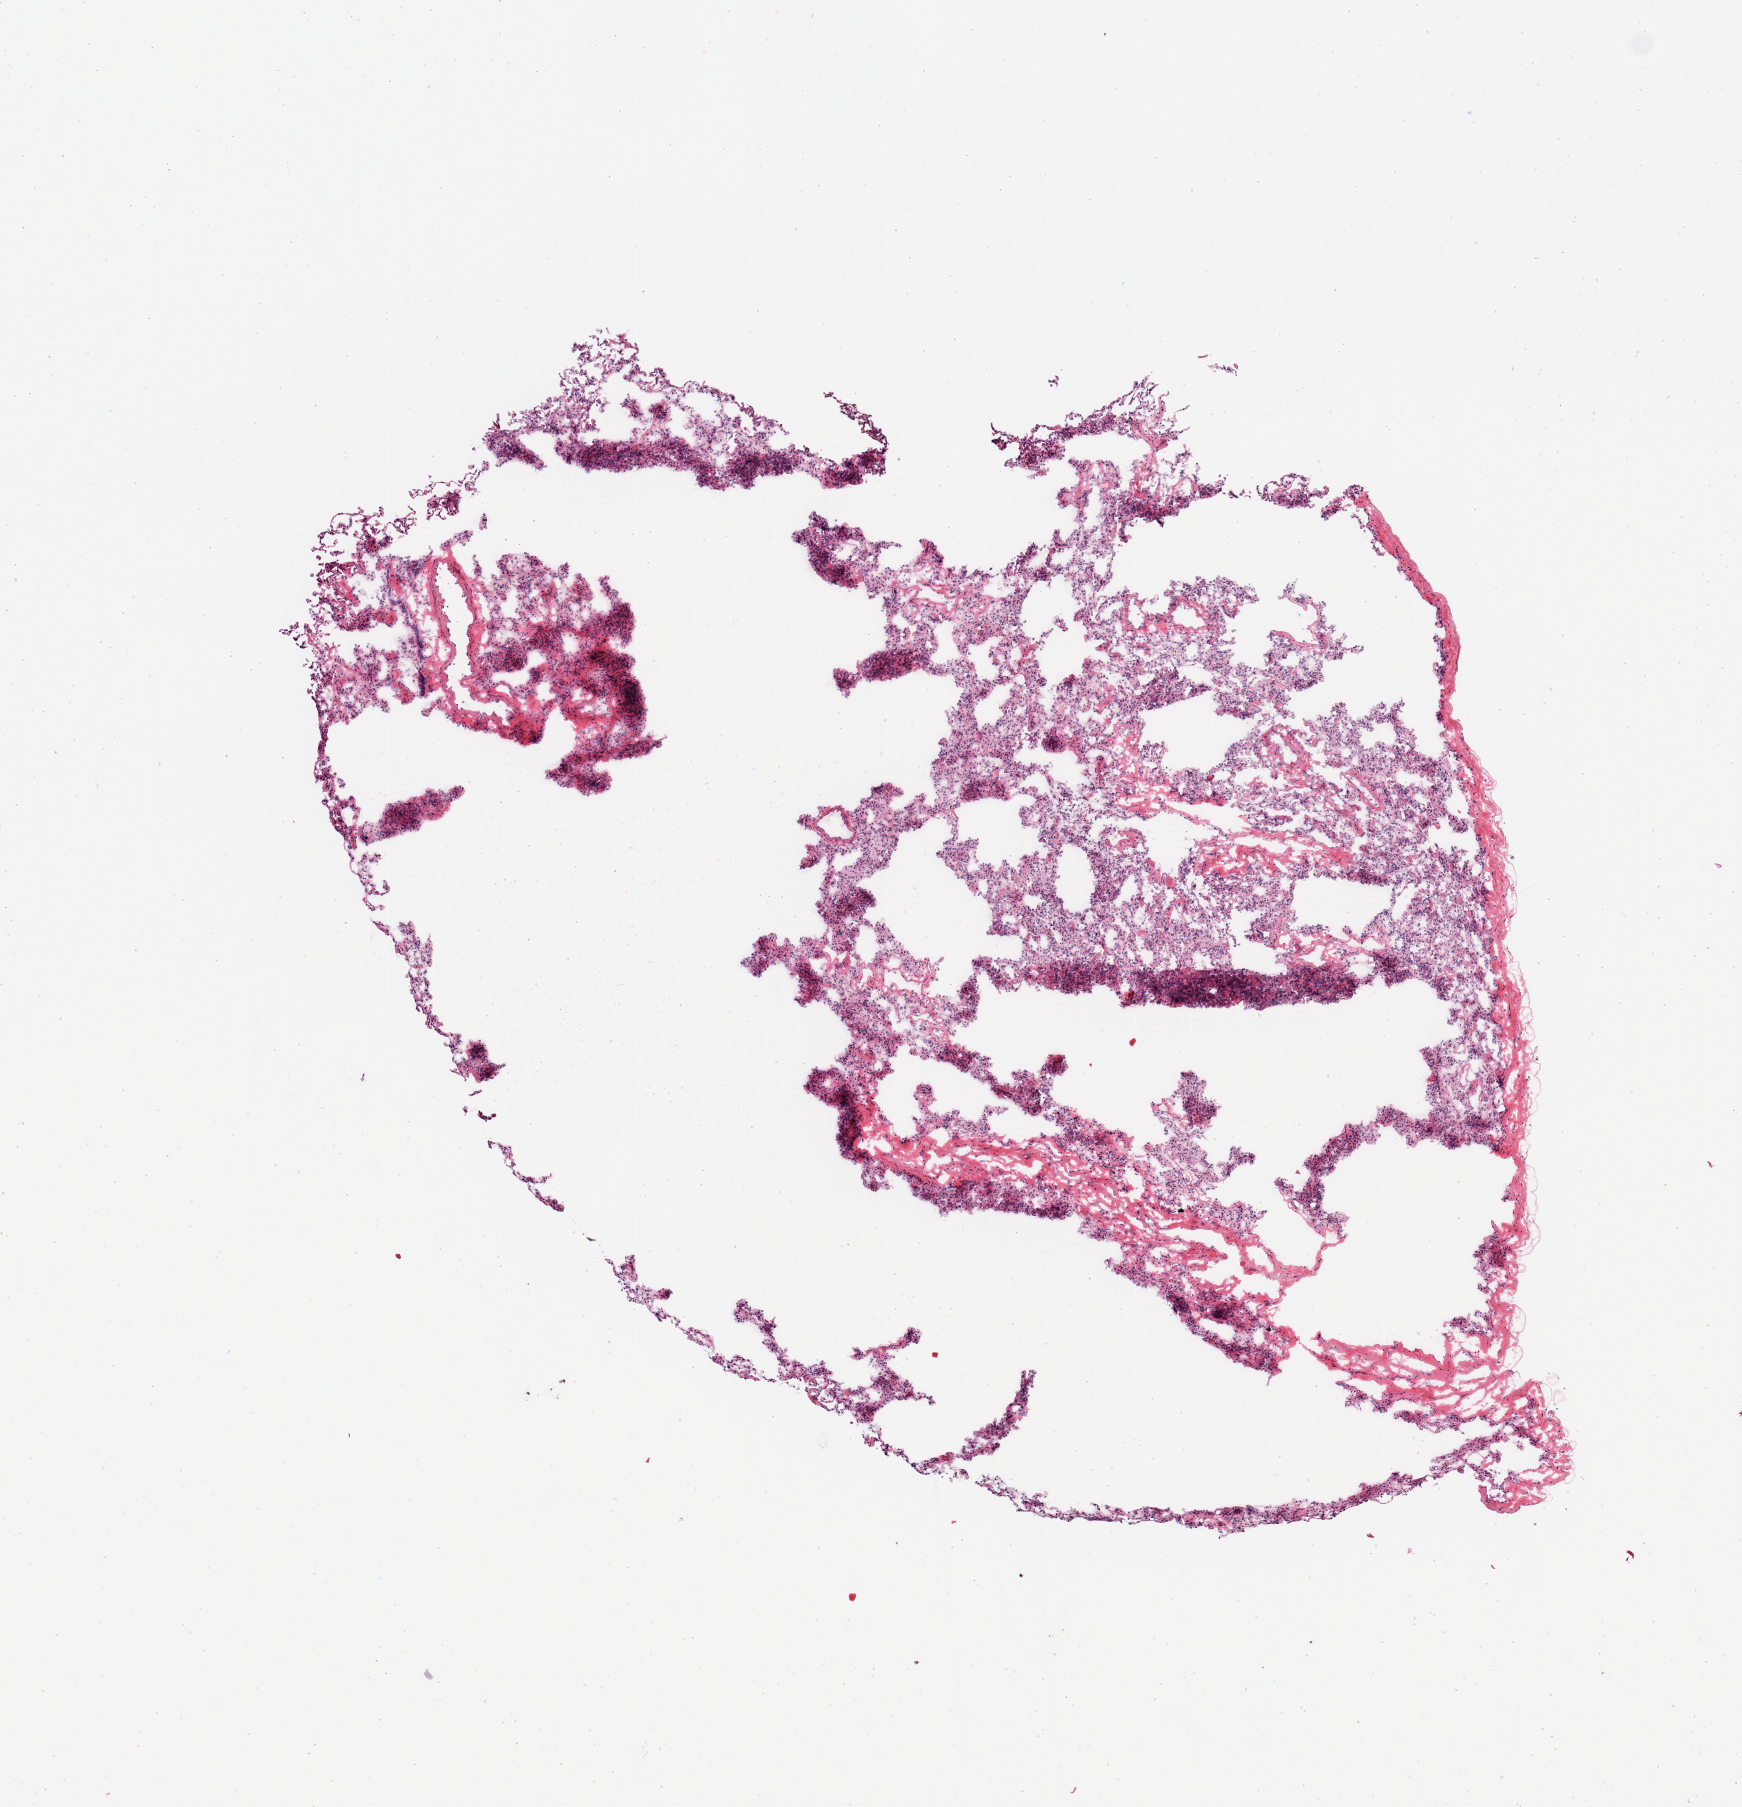
Digitized H&E-stained section, brightfield — whole scanned area (about 6.9 x 7.1 mm, acquisition: 20x scan) shown as a low-resolution overview, frozen section (dry ice), target tissue: lung, tissue donor sample.
Review note (as recorded): 1 piece; comparable to PAXgene sample.